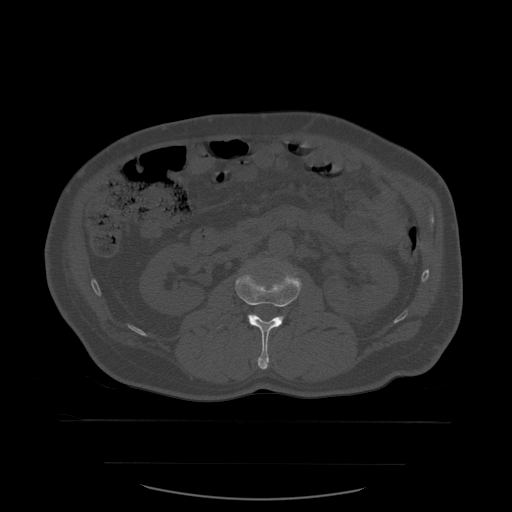
CT including the spine, one axial slice. Slice 215 of 590 in the series (ordered by position). Bone window (W 1800 / L 400 HU). 1.25 mm slice thickness. 512 × 512 image matrix, field of view 479 × 479 mm. Patient age 71 years. From the clinical record (not read from this slice): primary cancer: lung.
Annotated regions visible in this slice (semi-automatic segmentation, software-assisted and operator-edited):
- L2 vertebra: bounding box (x1, y1, x2, y2) in pixels: (235, 270, 302, 370)